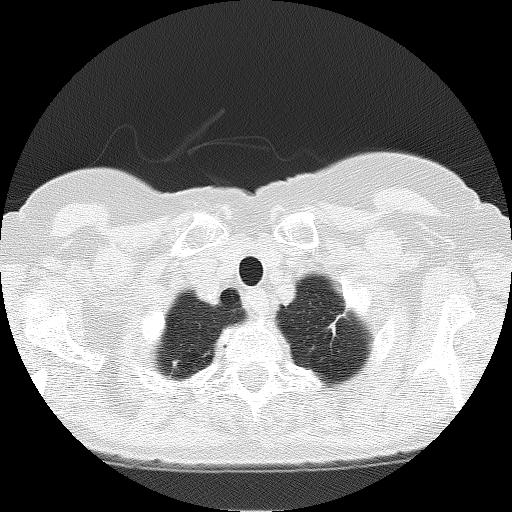
Low-dose screening chest CT, one axial slice; slice 156 of 166 in the series (ordered by position); lung window (W 1500 / L -600 HU); 2 mm slice thickness; 512 × 512 image matrix.
Outlined on this slice (expert manual segmentation):
- lesion 3 (nodule, upper lobe of left lung): box from (x=329, y=316) to (x=341, y=333) px